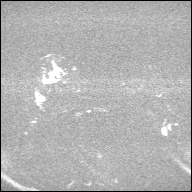
Breast MRI, one axial slice. Diffusion-weighted series; image 2 of 4 stored at this slice position (different b-values; order by instance number). 1.5 T. 4 mm slice thickness. 192 × 192 image matrix, field of view 360 × 360 mm. Female patient.
Annotated regions visible in this slice (manually delineated by an expert):
- tumour on diffusion-weighted imaging: bounding box [x1, y1, x2, y2] px = [54, 69, 58, 74]